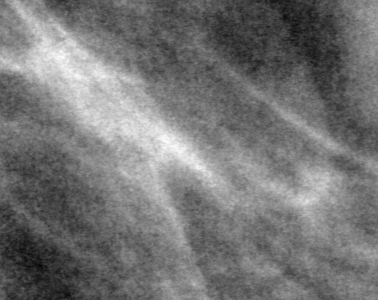
Crop from a digitized film mammogram around one marked abnormality; left breast; MLO view.
Finding: mass, shape oval, margins obscured; BI-RADS assessment category 0; pathology (as recorded): benign.